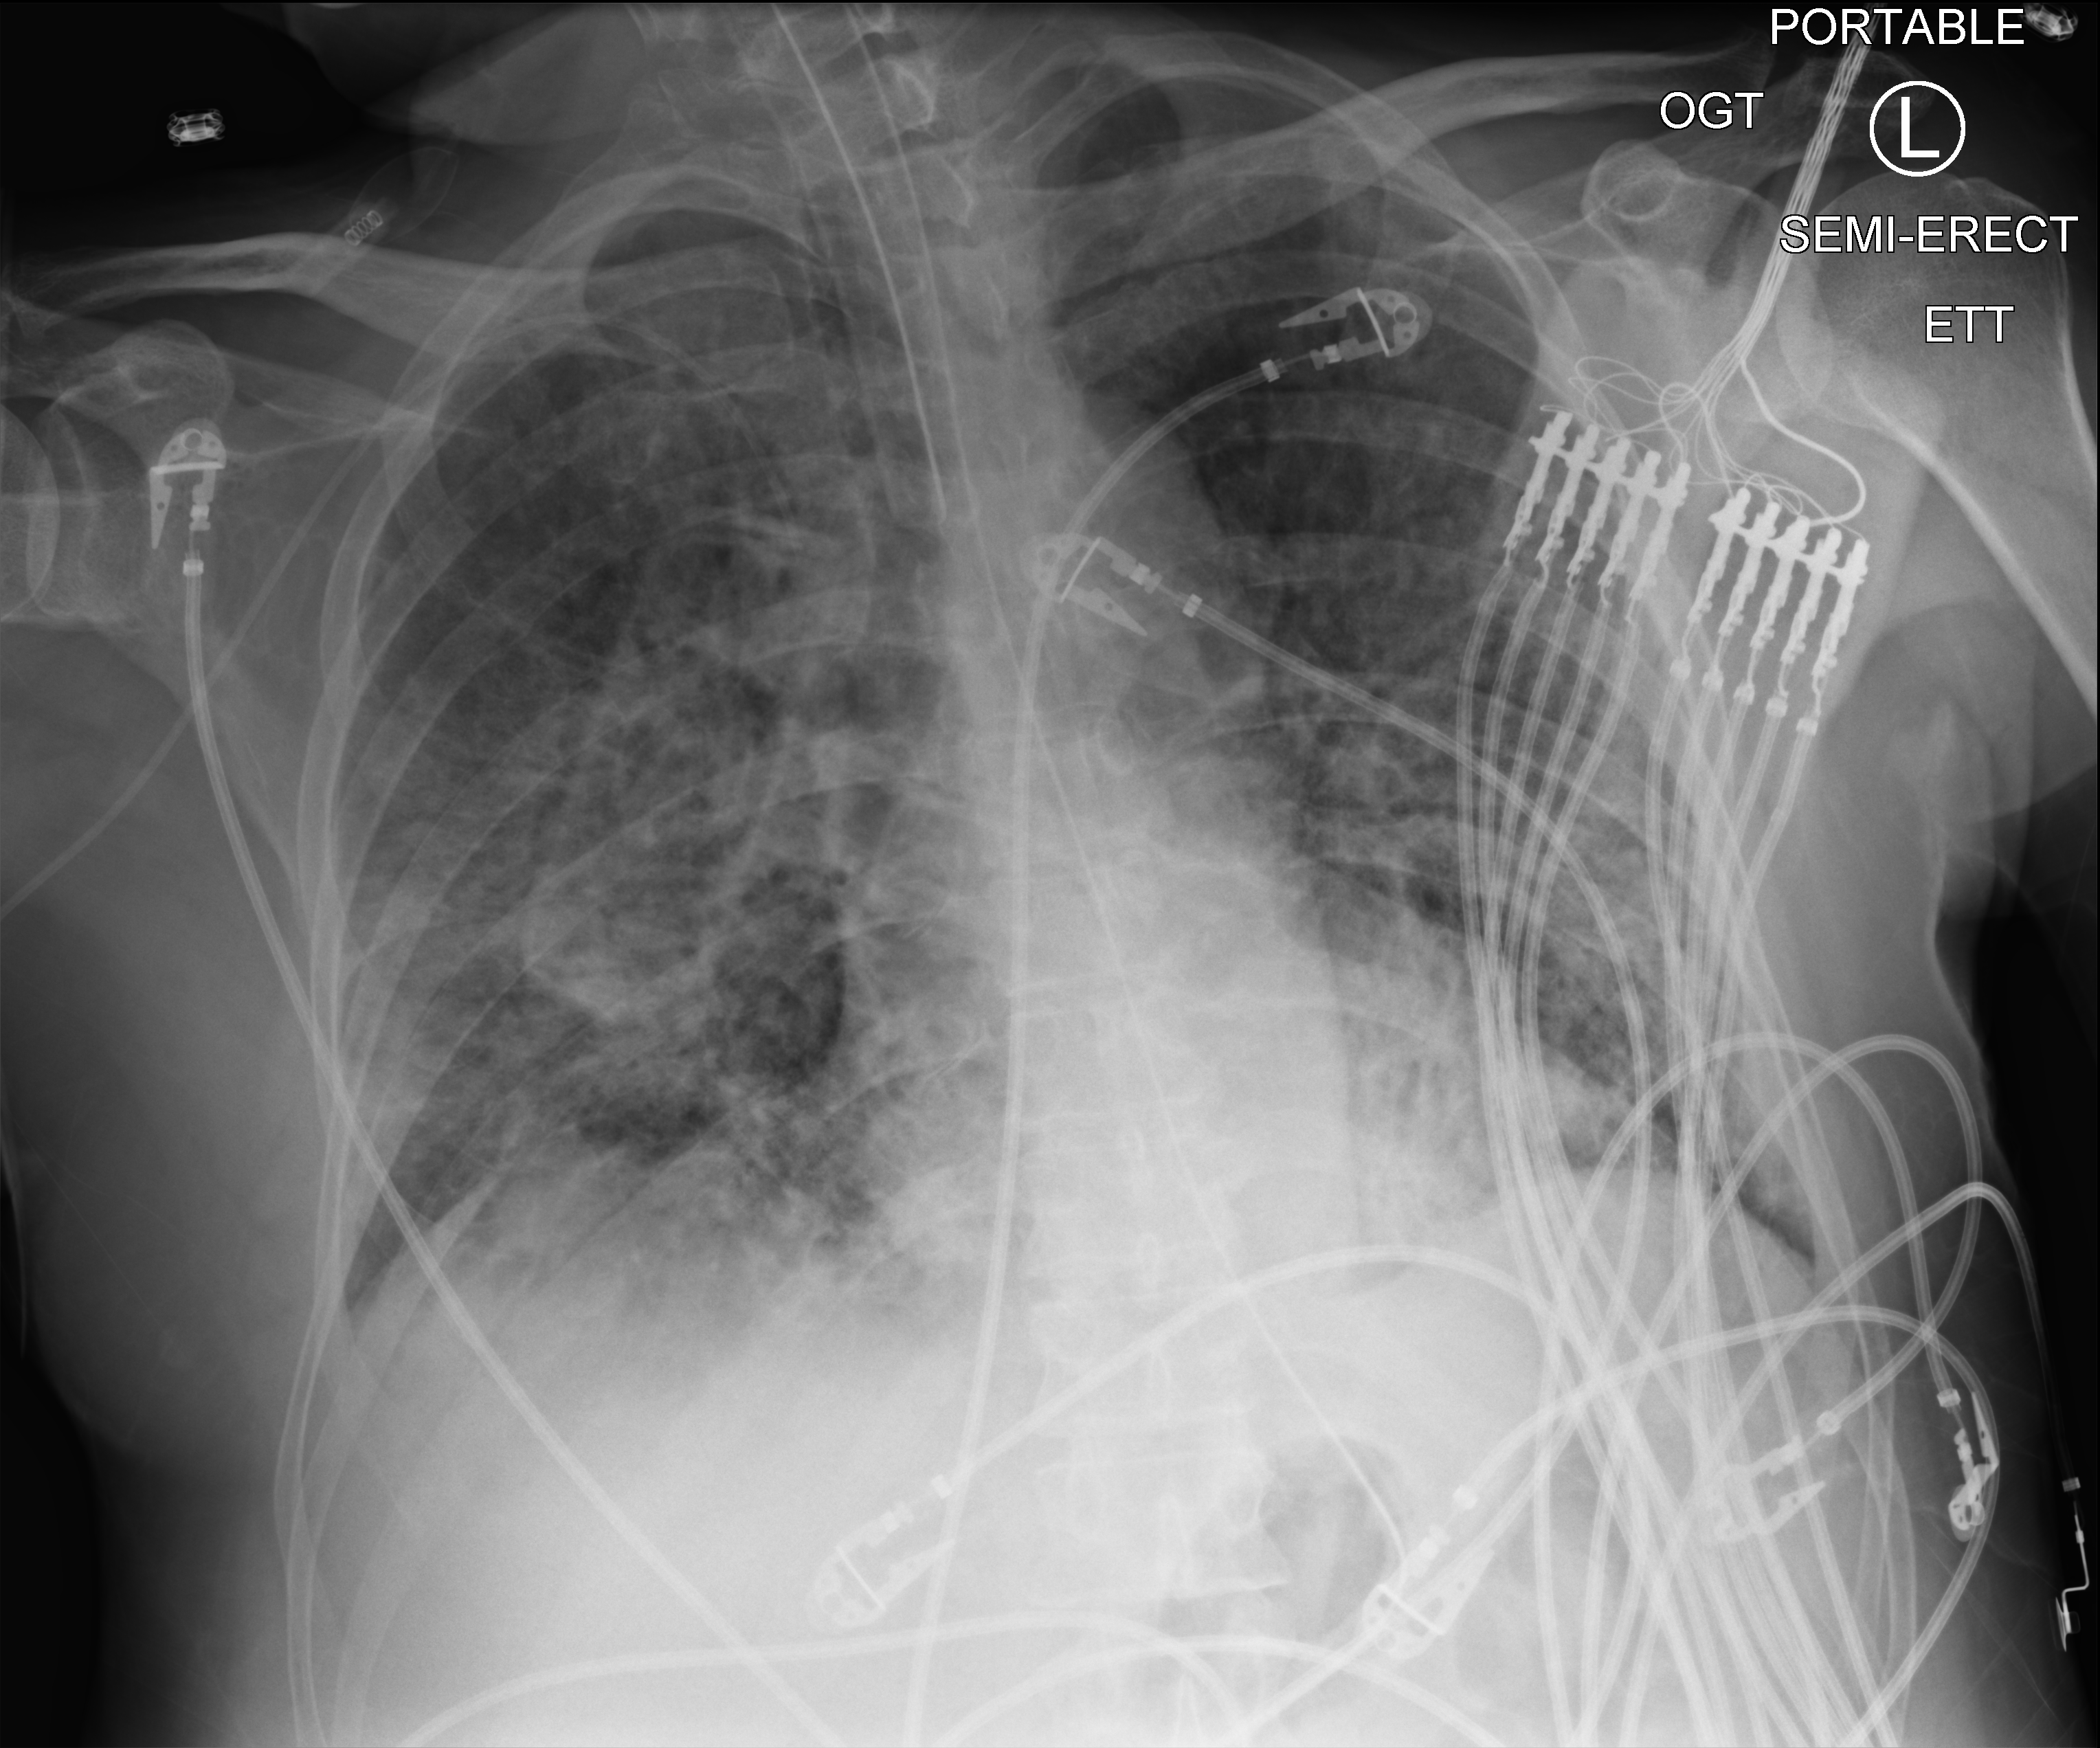
Portable chest radiograph; anteroposterior (AP) projection. Patient hospitalised with COVID-19; male, aged 60–74 years.
Admission-level facts for this patient (not findings on this image; timing relative to this image not recorded): mechanically ventilated during this hospital stay: yes; admitted to intensive care during this hospital stay: yes.